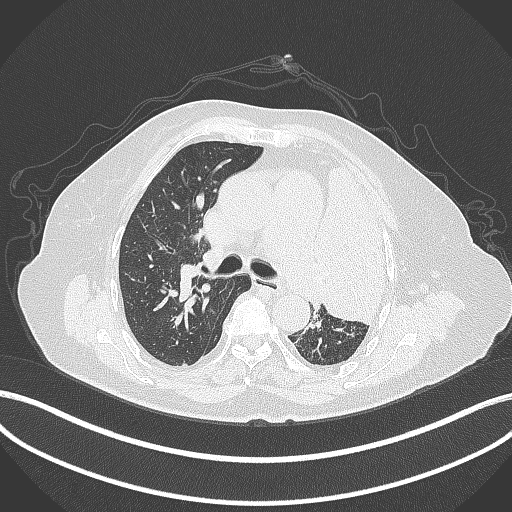
Chest CT, one axial slice. Position 247 of 399 along the scan axis. Lung window (W 1500 / L -600 HU). 1 mm slice thickness. 512 × 512 image matrix, field of view 400 × 400 mm. Patient: female, 75 years. From the clinical record (not read from this slice): clinical TNM (as recorded): T3 N3 M1.
Annotated regions visible in this slice (bounding box drawn by a radiologist):
- lung tumour (recorded histology: adenocarcinoma): box from (x=316, y=153) to (x=391, y=324) px